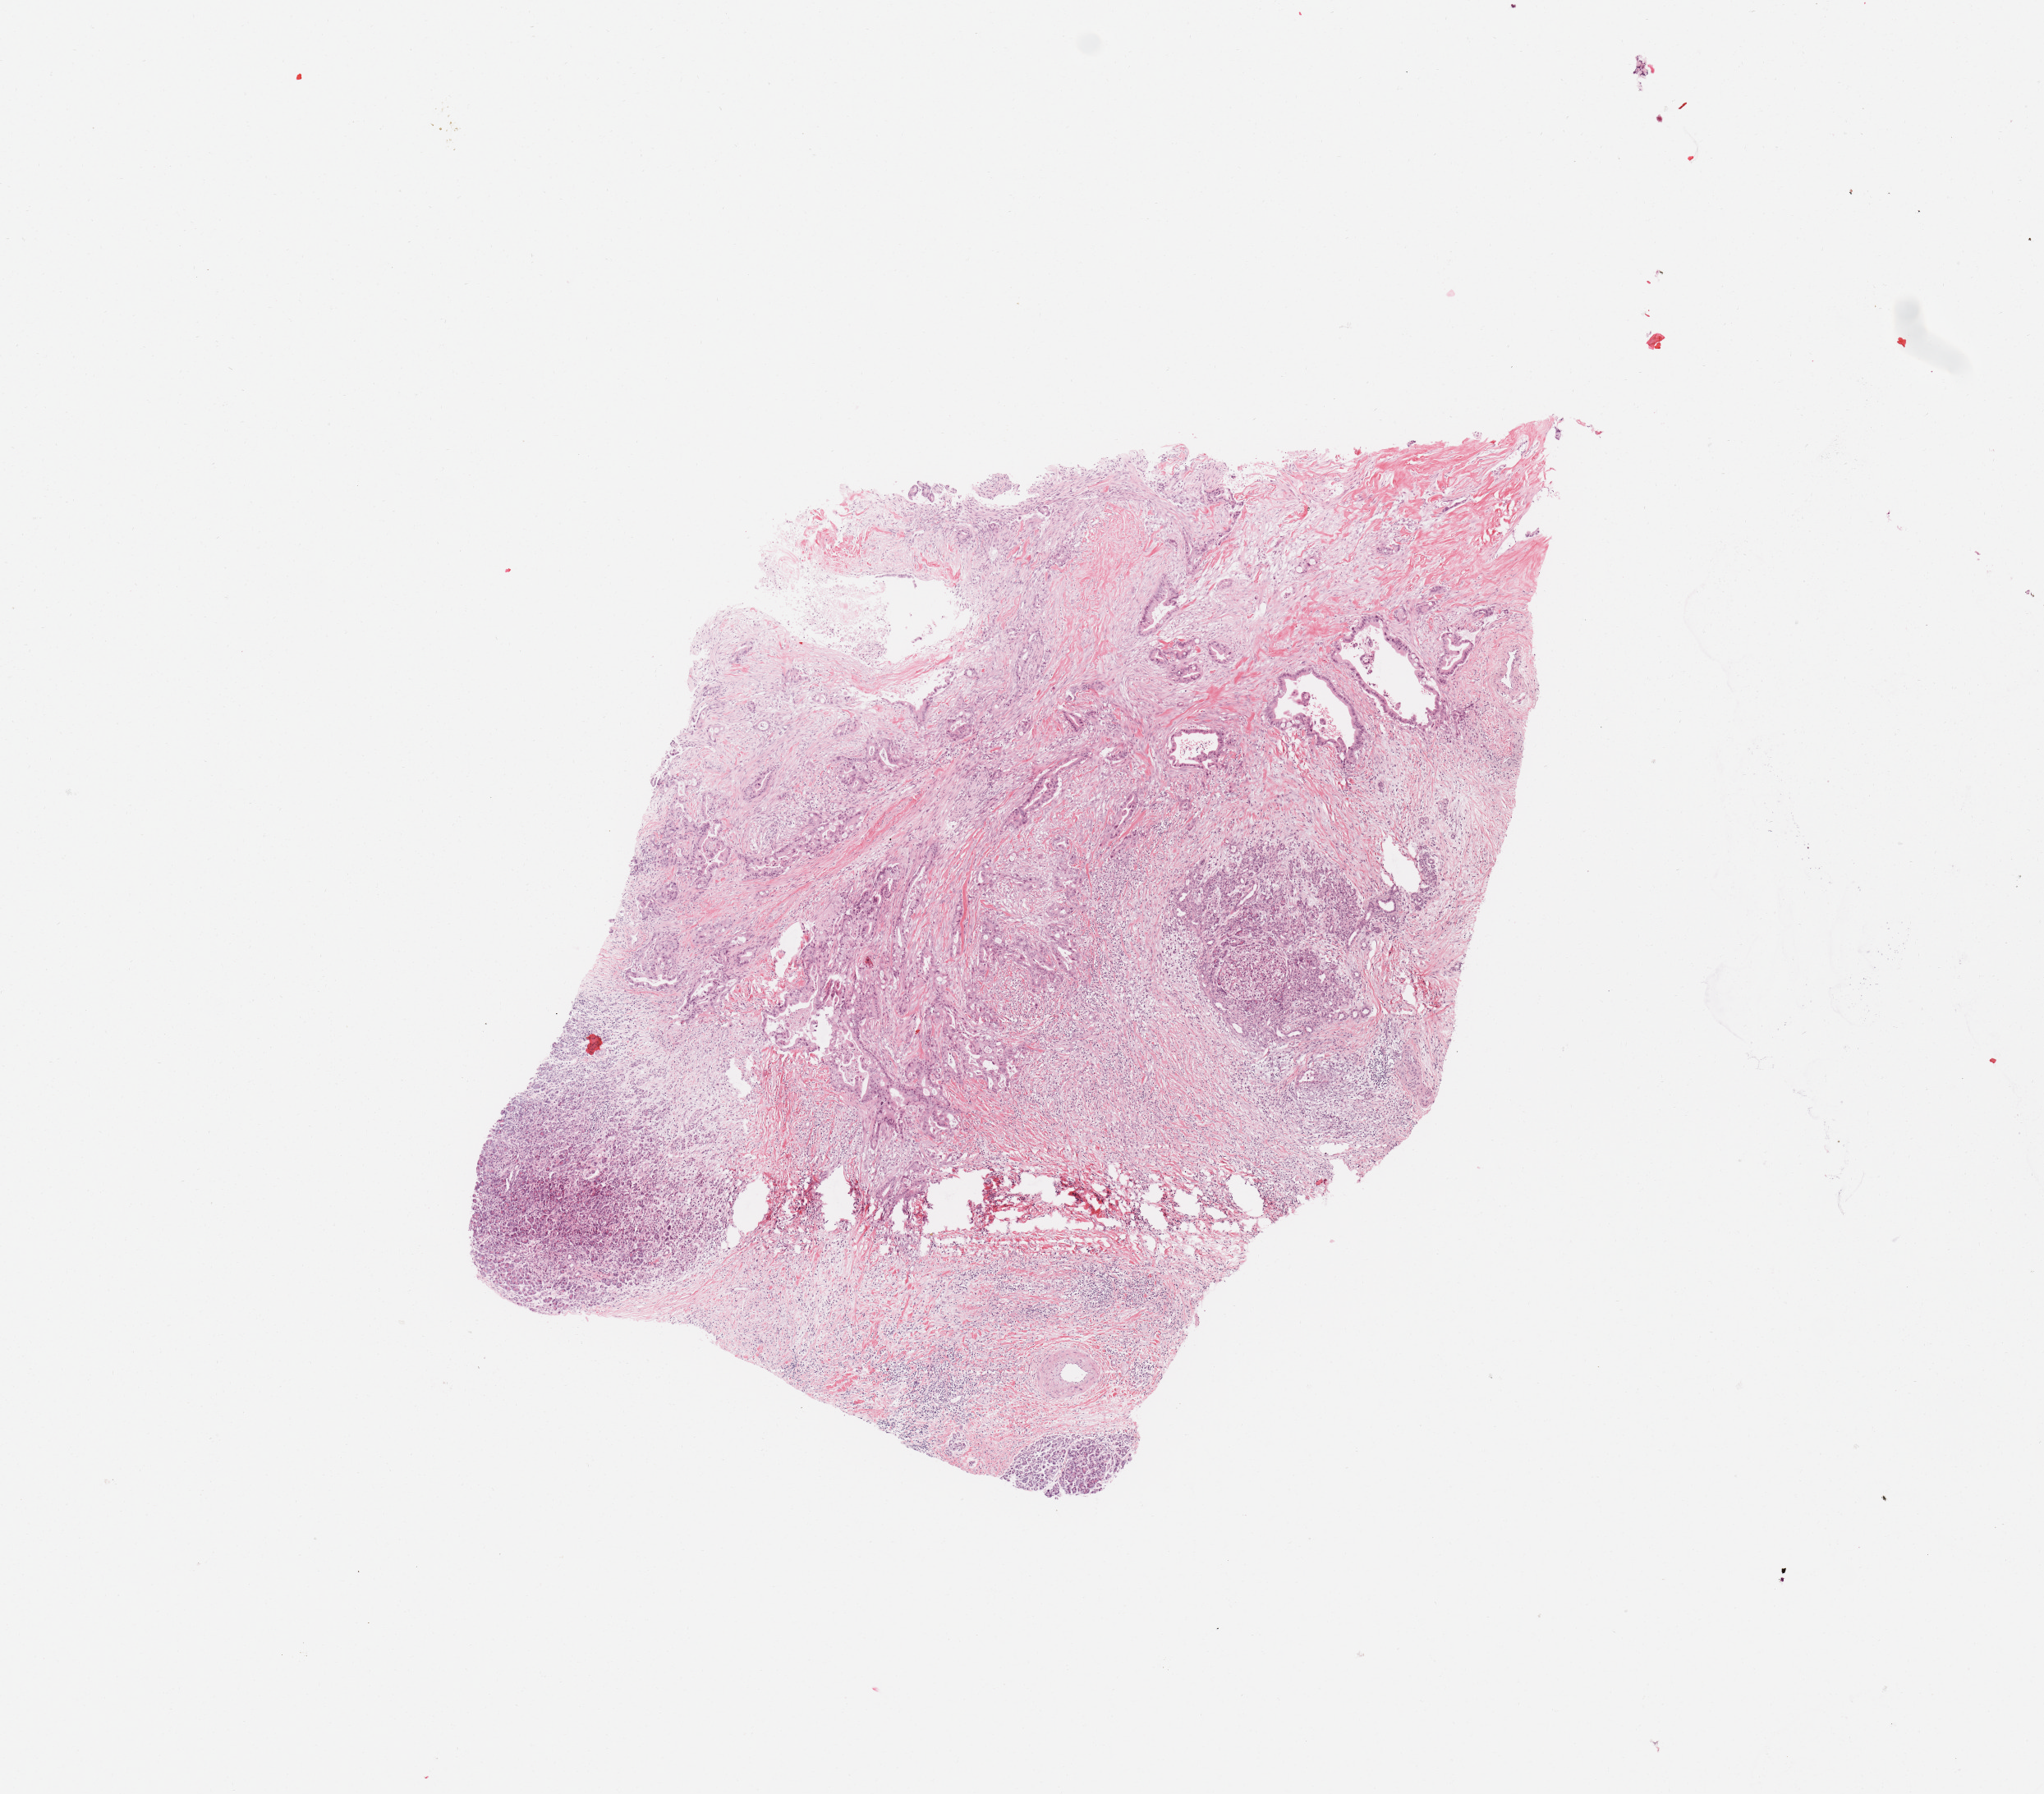
Digitized Hematoxylin and eosin (H&E) stained tissue section (whole slide) — low-resolution overview of the scanned area, about 9.8 x 8.6 mm. Tumour tissue sample, sampled site: pancreas. 59-year-old female patient. Histologic grade: G2 (moderately differentiated). Composition of this section per pathologist review: tumour nuclei 20%, necrosis 0%.
* primary tumour site (as recorded): body
* histologic diagnosis: Infiltrating duct carcinoma, NOS
* AJCC pathologic stage: IIB